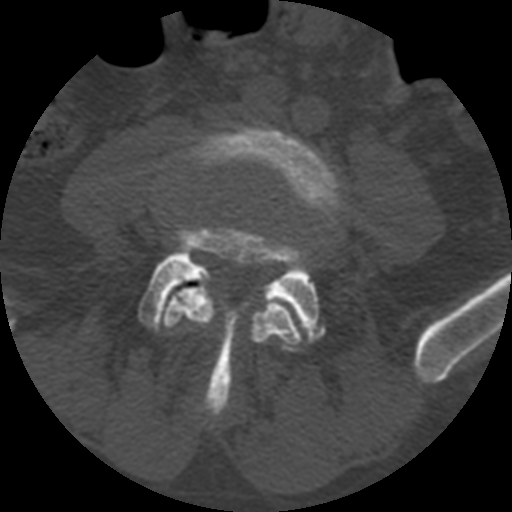
CT including the spine, one axial slice; slice 267 of 399 in the series (ordered by position); reconstruction kernel STANDARD; 120 kVp; bone window (W 1800 / L 400 HU); 1.25 mm slice thickness; 512 × 512 image matrix, field of view 160 × 160 mm. Patient age 71 years. From the clinical record (not read from this slice): primary cancer: prostate.
Outlined on this slice (semi-automatically segmented with operator editing):
- L4 vertebra: bounding box (x1, y1, x2, y2) in pixels: (162, 125, 343, 350)
- L5 vertebra: (137, 226, 326, 416)